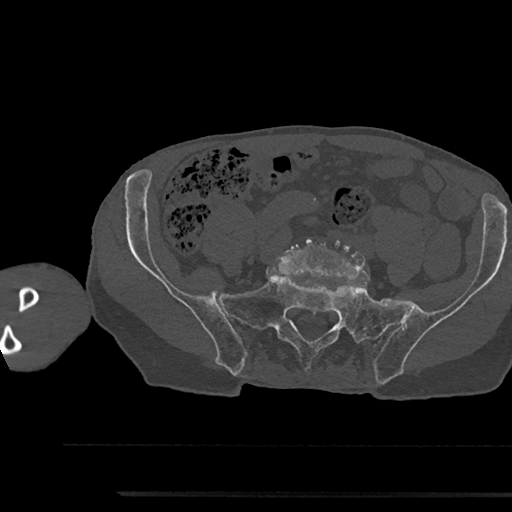
CT including the spine, one axial slice. Slice 304 of 797 in the series (ordered by position). 120 kVp. Bone window (W 1800 / L 400 HU). 512 × 512 image matrix, field of view 367 × 367 mm. Patient: male, 79 years. Case-level facts recorded for this patient, not image findings: primary cancer: prostate.
Outlined on this slice (semi-automatically segmented with operator editing):
- L5 vertebra: bounding box [x1, y1, x2, y2] px = [277, 235, 370, 280]